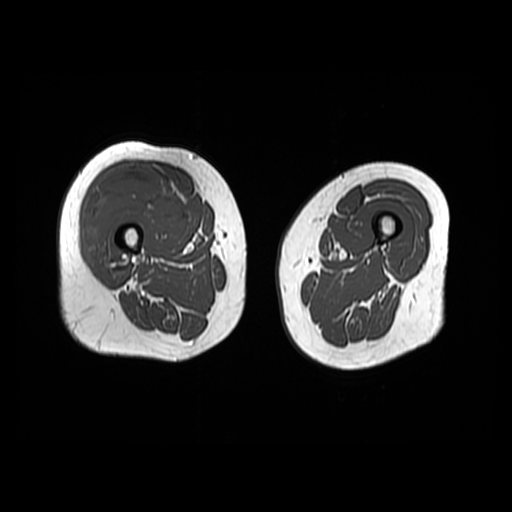
MRI of an extremity soft-tissue mass, one axial slice. Position 21 of 48 along the scan axis. 6 mm slice thickness. 512 × 512 image matrix, field of view 440 × 440 mm. Female patient. Case-level facts recorded for this patient, not image findings: histological type: pleiomorphic undifferentiated sarcoma; grade: high; site of the primary tumour: right quadricep.
Annotated regions visible in this slice (manually delineated by an expert):
- gross tumour volume including surrounding oedema: bounding box <84,166,181,261> (left, top, right, bottom; pixels)
- gross tumour volume (mass): <84,166,181,261>